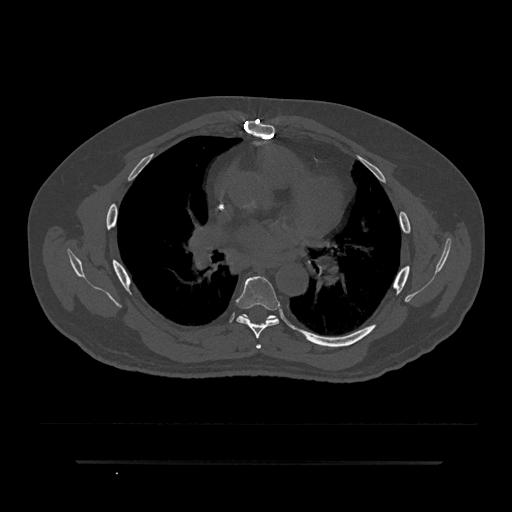
CT including the spine, one axial slice; position 517 of 797 along the scan axis; bone window (W 1800 / L 400 HU); 0.5 mm slice thickness; 512 × 512 image matrix, field of view 464 × 464 mm. Male patient, age 59 years. From the clinical record (not read from this slice): primary cancer: bile ducts; vertebrae with lytic lesions (as recorded): T10.
Annotated regions visible in this slice (semi-automatic segmentation, software-assisted and operator-edited):
- T5 vertebra: bounding box <256,344,262,349> (left, top, right, bottom; pixels)
- T6 vertebra: <236,276,280,339>